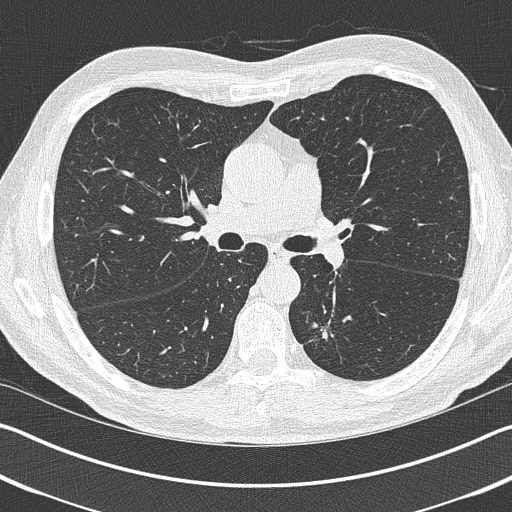
Low-dose screening chest CT, one axial slice; position 248 of 402 along the scan axis; reconstruction kernel B50f; lung window (W 1500 / L -600 HU); 1 mm slice thickness; 512 × 512 image matrix, field of view 340 × 340 mm.
Structures marked on this image (outlined manually by an expert reader):
- lesion 1 (tumor, lower lobe of left lung): bounding box (x1, y1, x2, y2) in pixels: (312, 323, 333, 339)